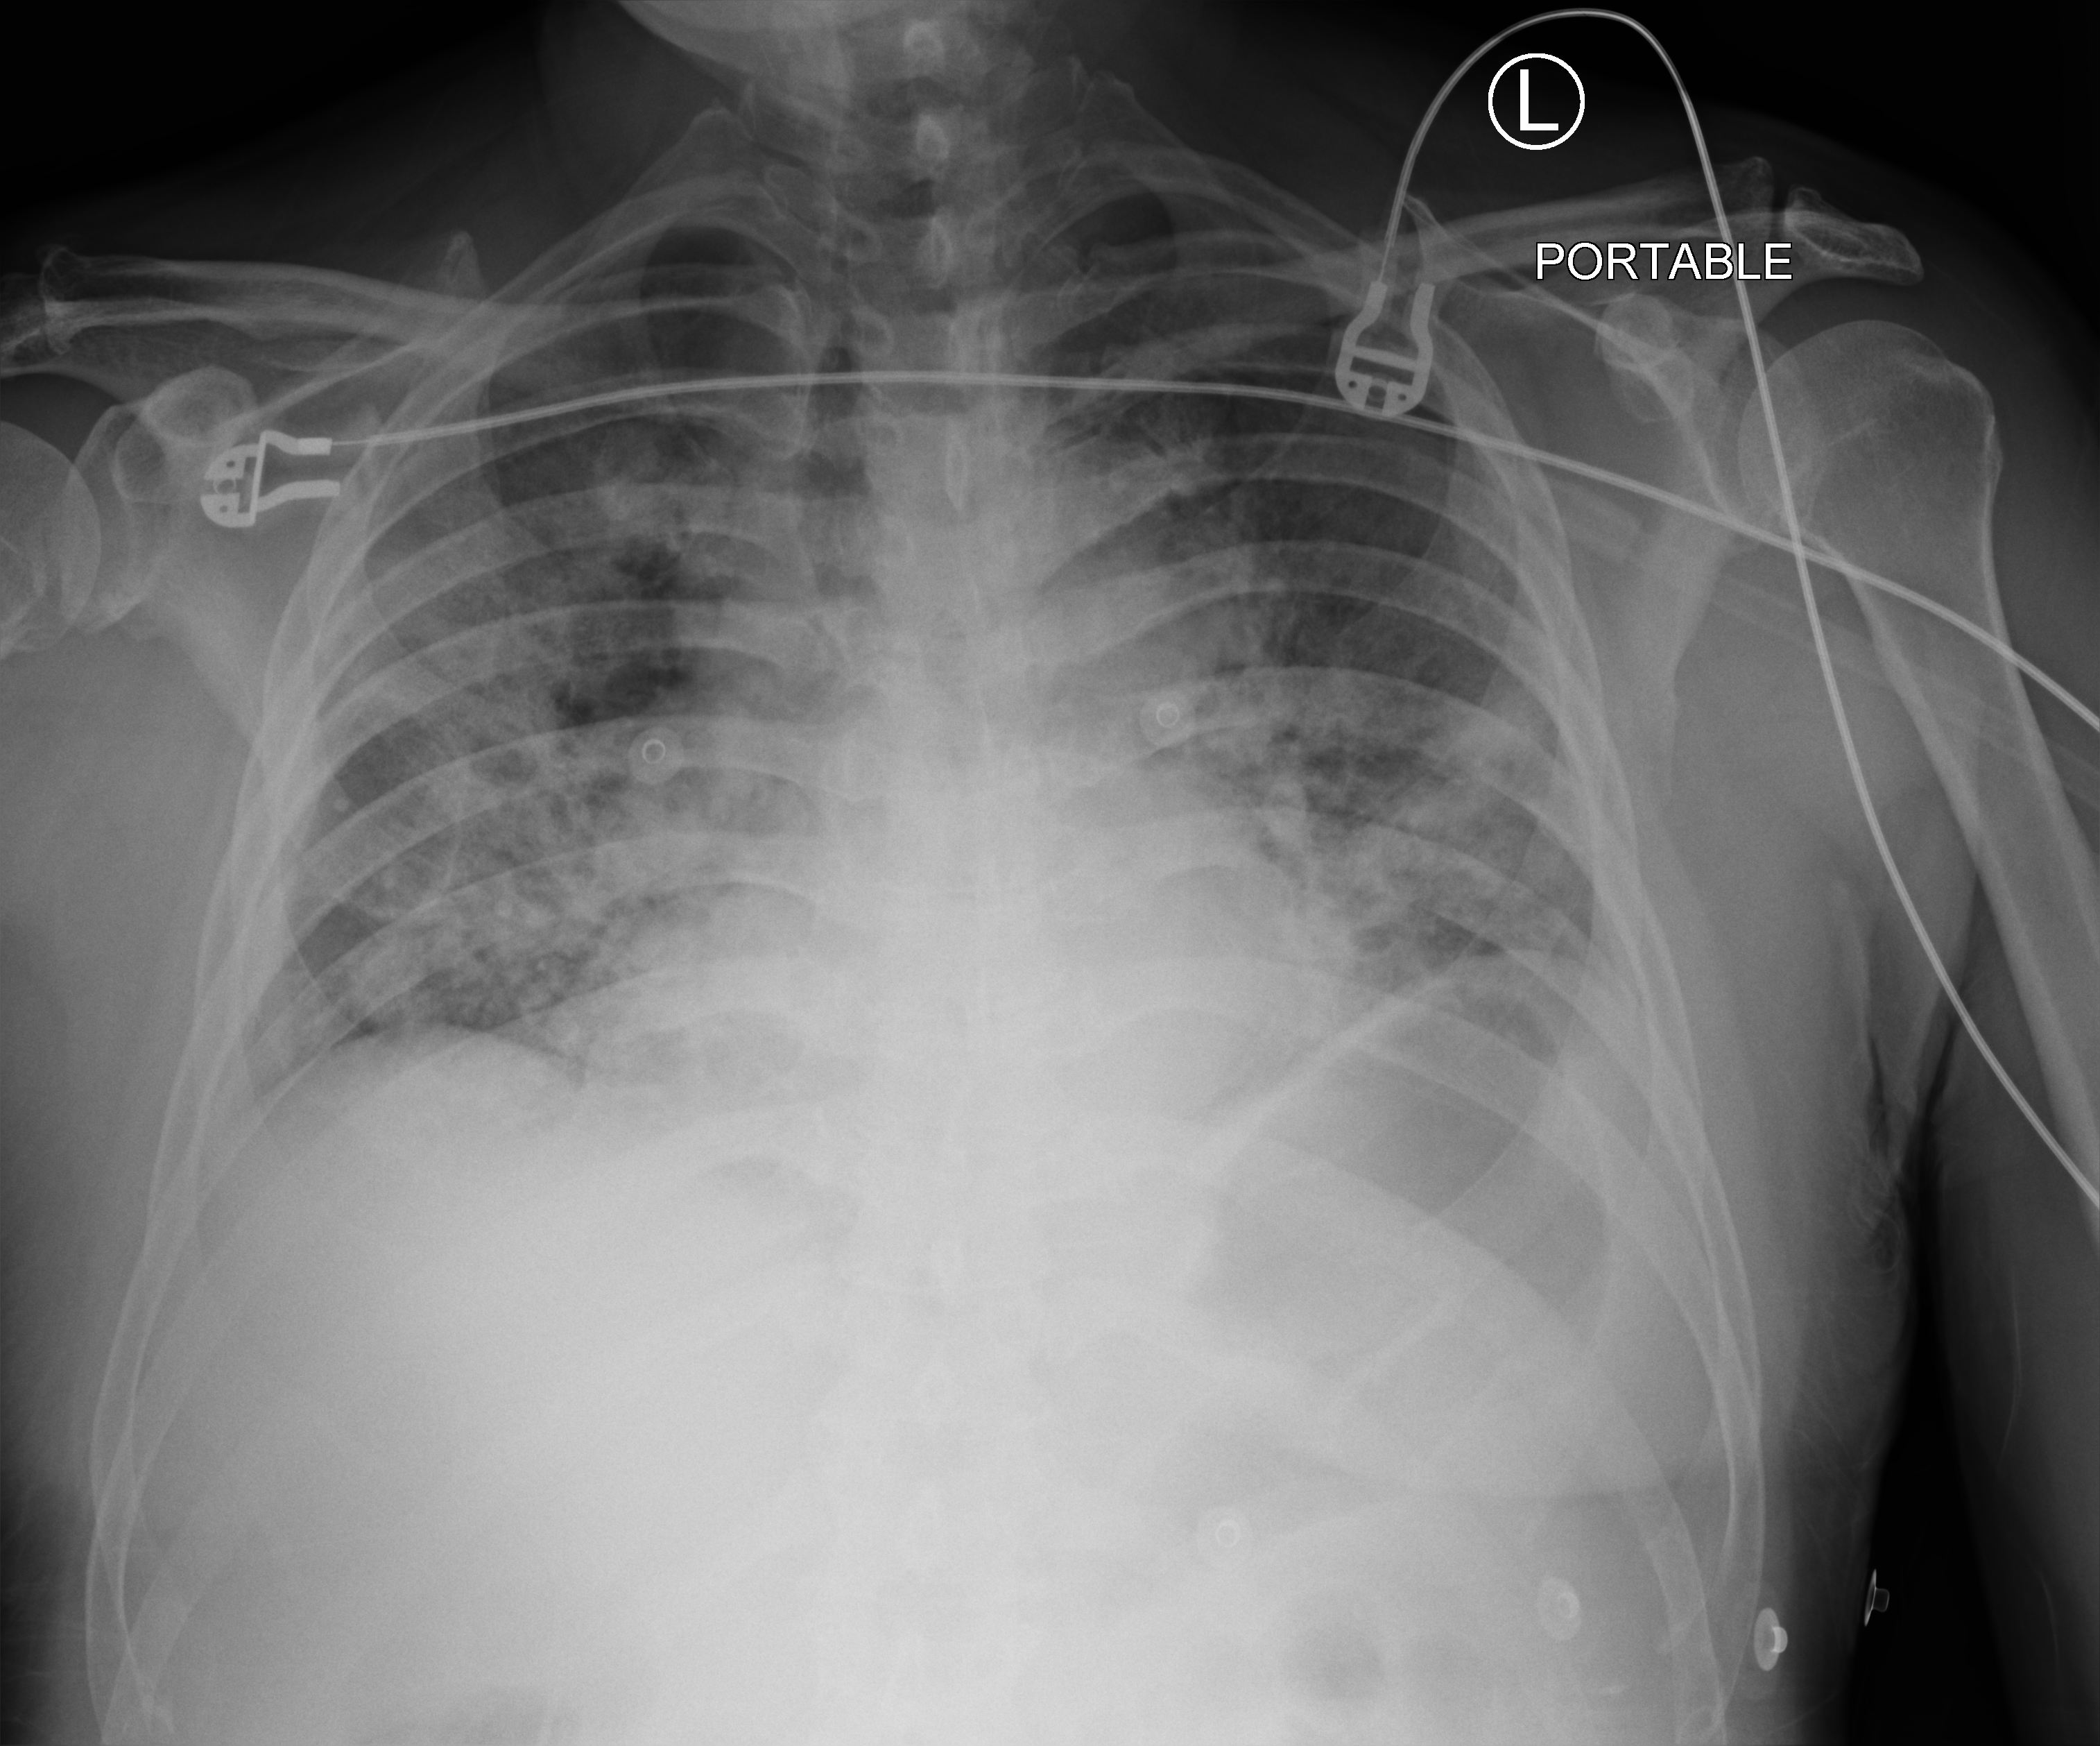
Chest X-ray (portable); anteroposterior (AP) projection. Male patient hospitalised with COVID-19, age 60–74 years.
From the hospital-stay record, not from the radiograph (when in the stay this image was taken is not recorded): length of hospital stay: 28 days.